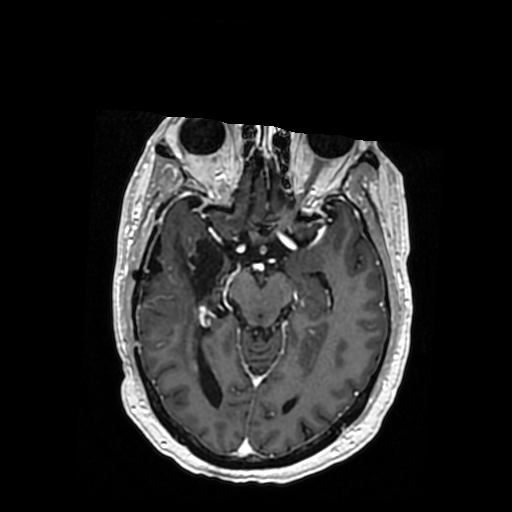
Brain MRI from a brain-tumour surgery series, one axial slice. Position 210 of 364 along the scan axis. T1-weighted post-contrast. 0.5 mm slice thickness. 512 × 512 image matrix, field of view 260 × 260 mm. From the clinical record (not read from this slice): histopathology: Oligodendroglioma; WHO grade: 3; IDH mutation: yes.
Structures marked on this image (expert manual segmentation):
- previous resection cavity: box from (x=149, y=235) to (x=237, y=301) px